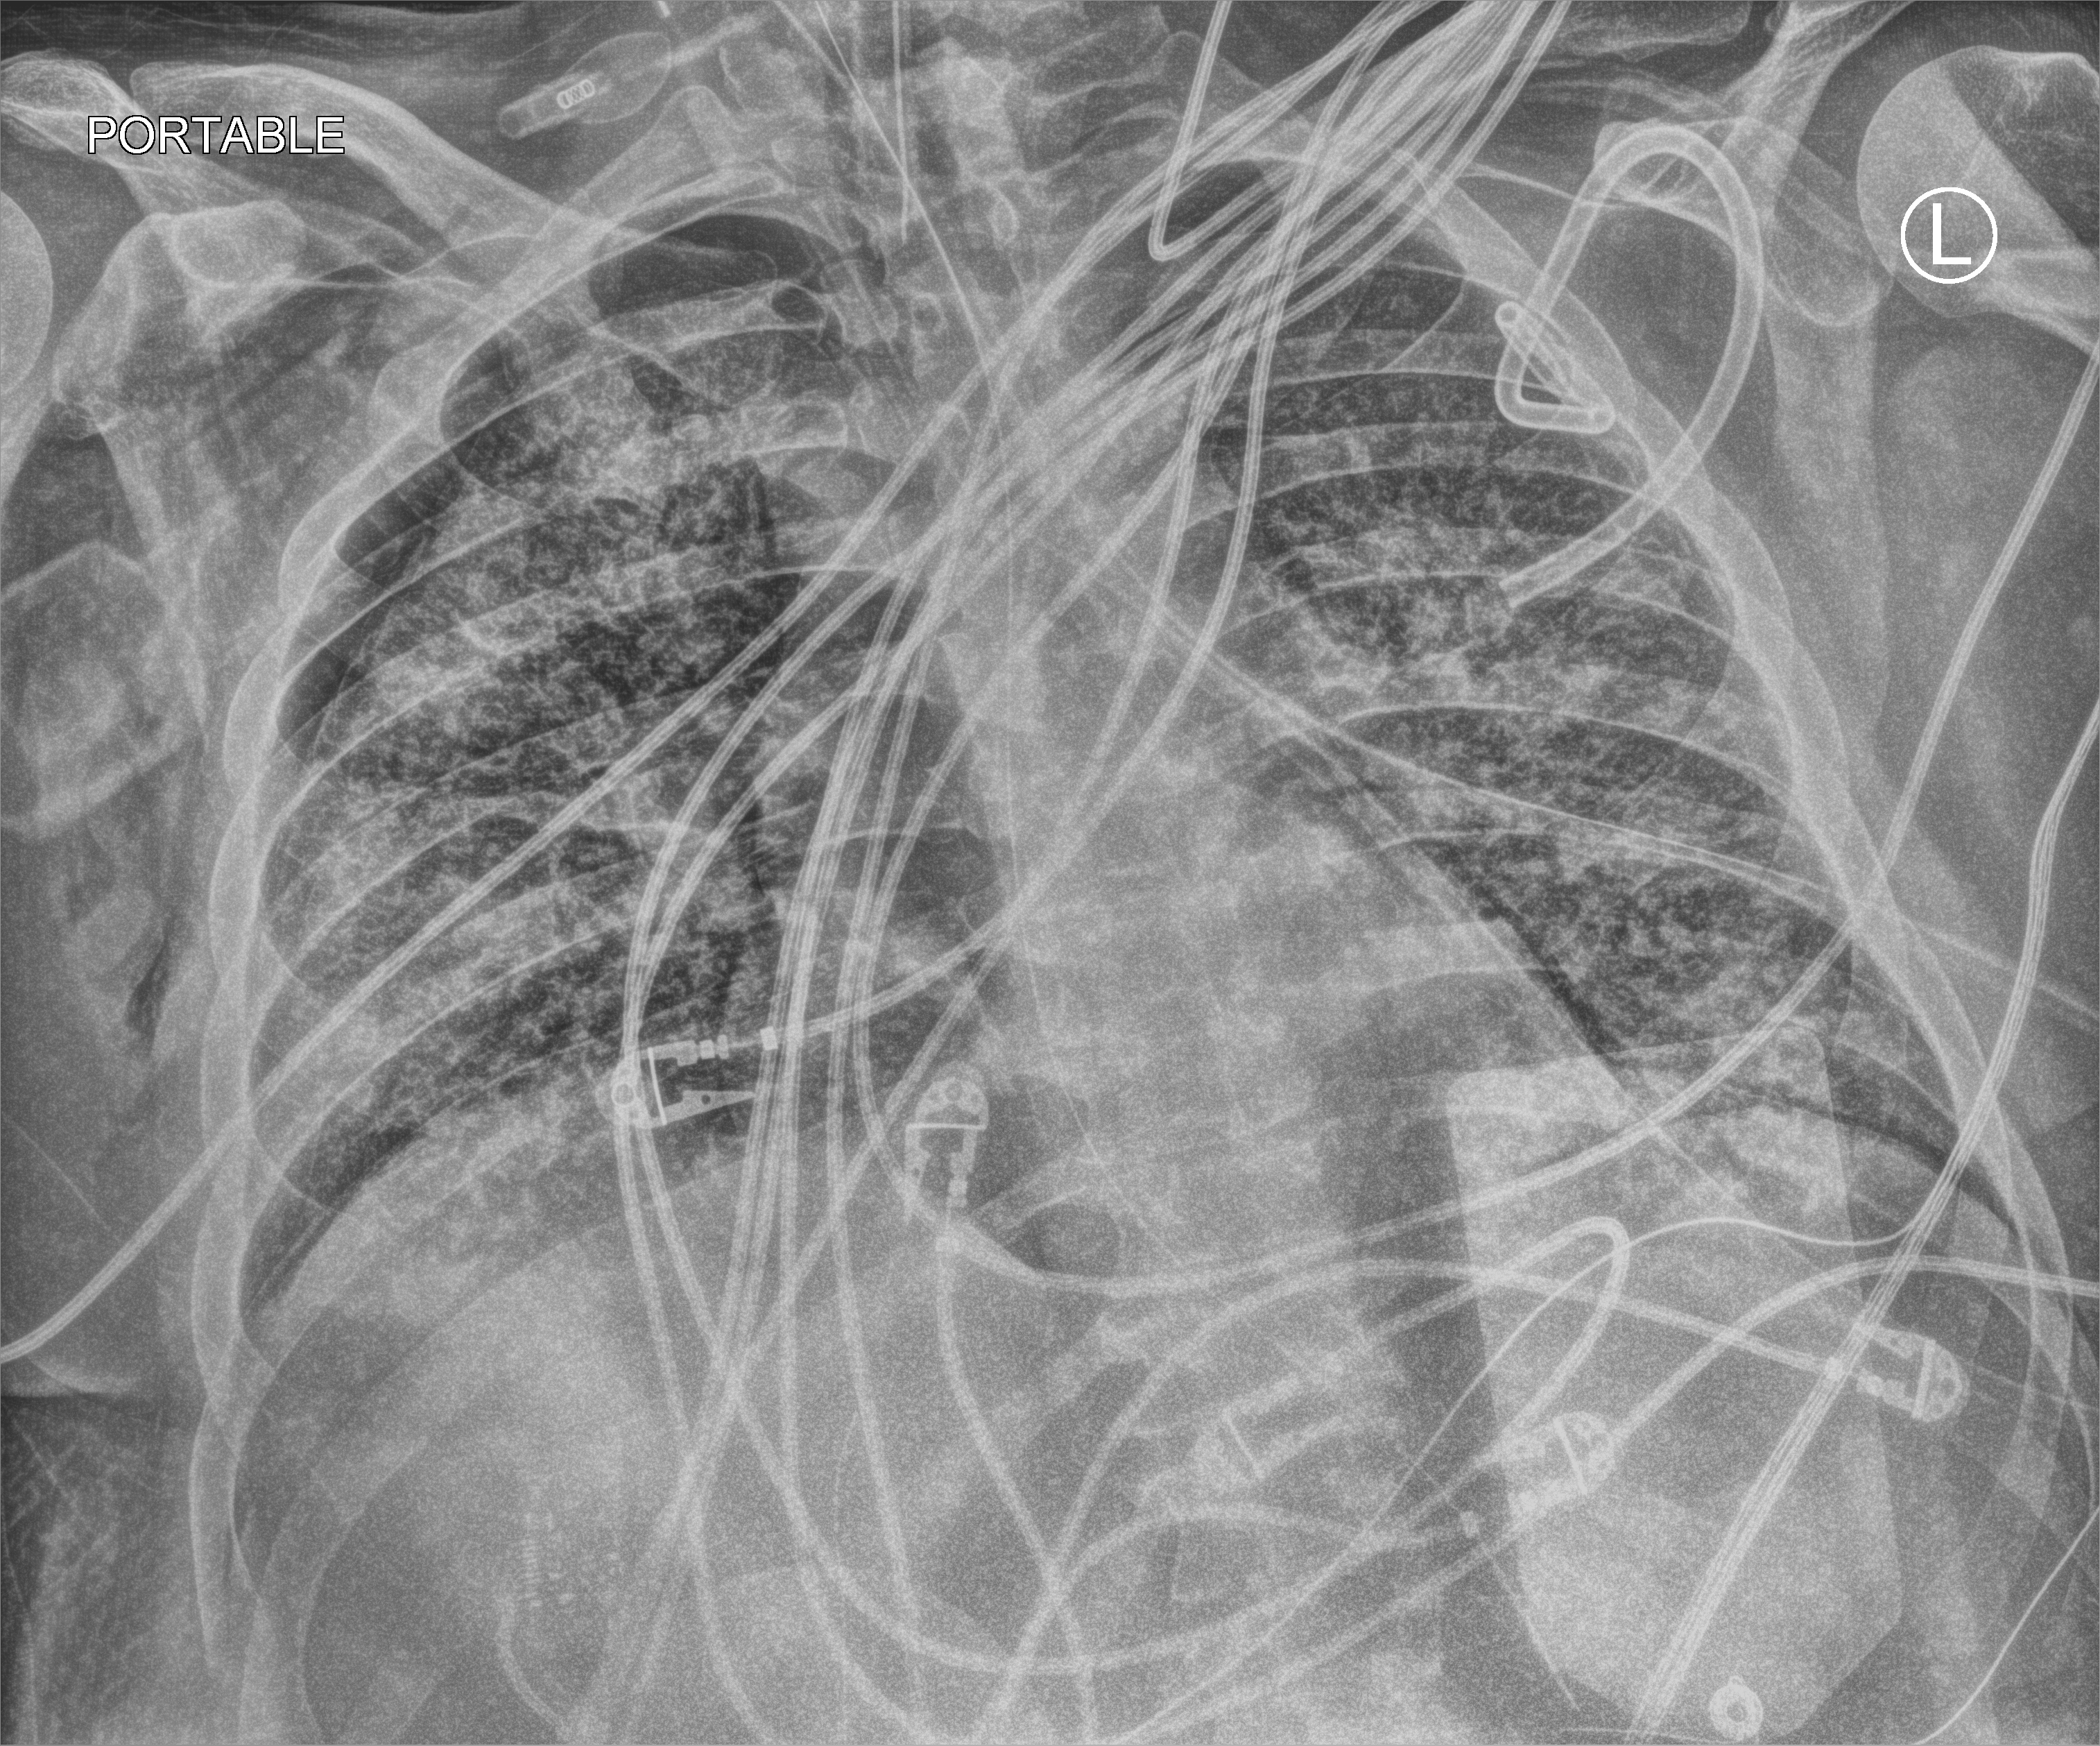
Chest X-ray (portable), anteroposterior (AP) projection. Patient hospitalised with COVID-19, aged 18–59 years.
Admission-level facts for this patient (not findings on this image; timing relative to this image not recorded):
- length of hospital stay: 31 days
- admitted to intensive care during this hospital stay: yes